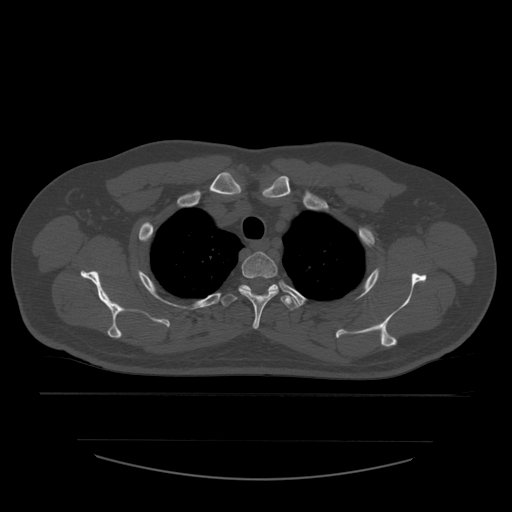
CT including the spine, one axial slice. Slice 445 of 532 in the series (ordered by position). Reconstruction kernel STANDARD. 120 kVp. Bone window (W 1800 / L 400 HU). 1.25 mm slice thickness. 512 × 512 image matrix, field of view 441 × 441 mm. Patient age 44 years. Case-level facts recorded for this patient, not image findings: primary cancer: soft tissue sarcoma.
Structures marked on this image (semi-automatically segmented with operator editing):
- T2 vertebra: box from (x=239, y=252) to (x=279, y=329) px
- T3 vertebra: (x=220, y=284)–(x=299, y=311)